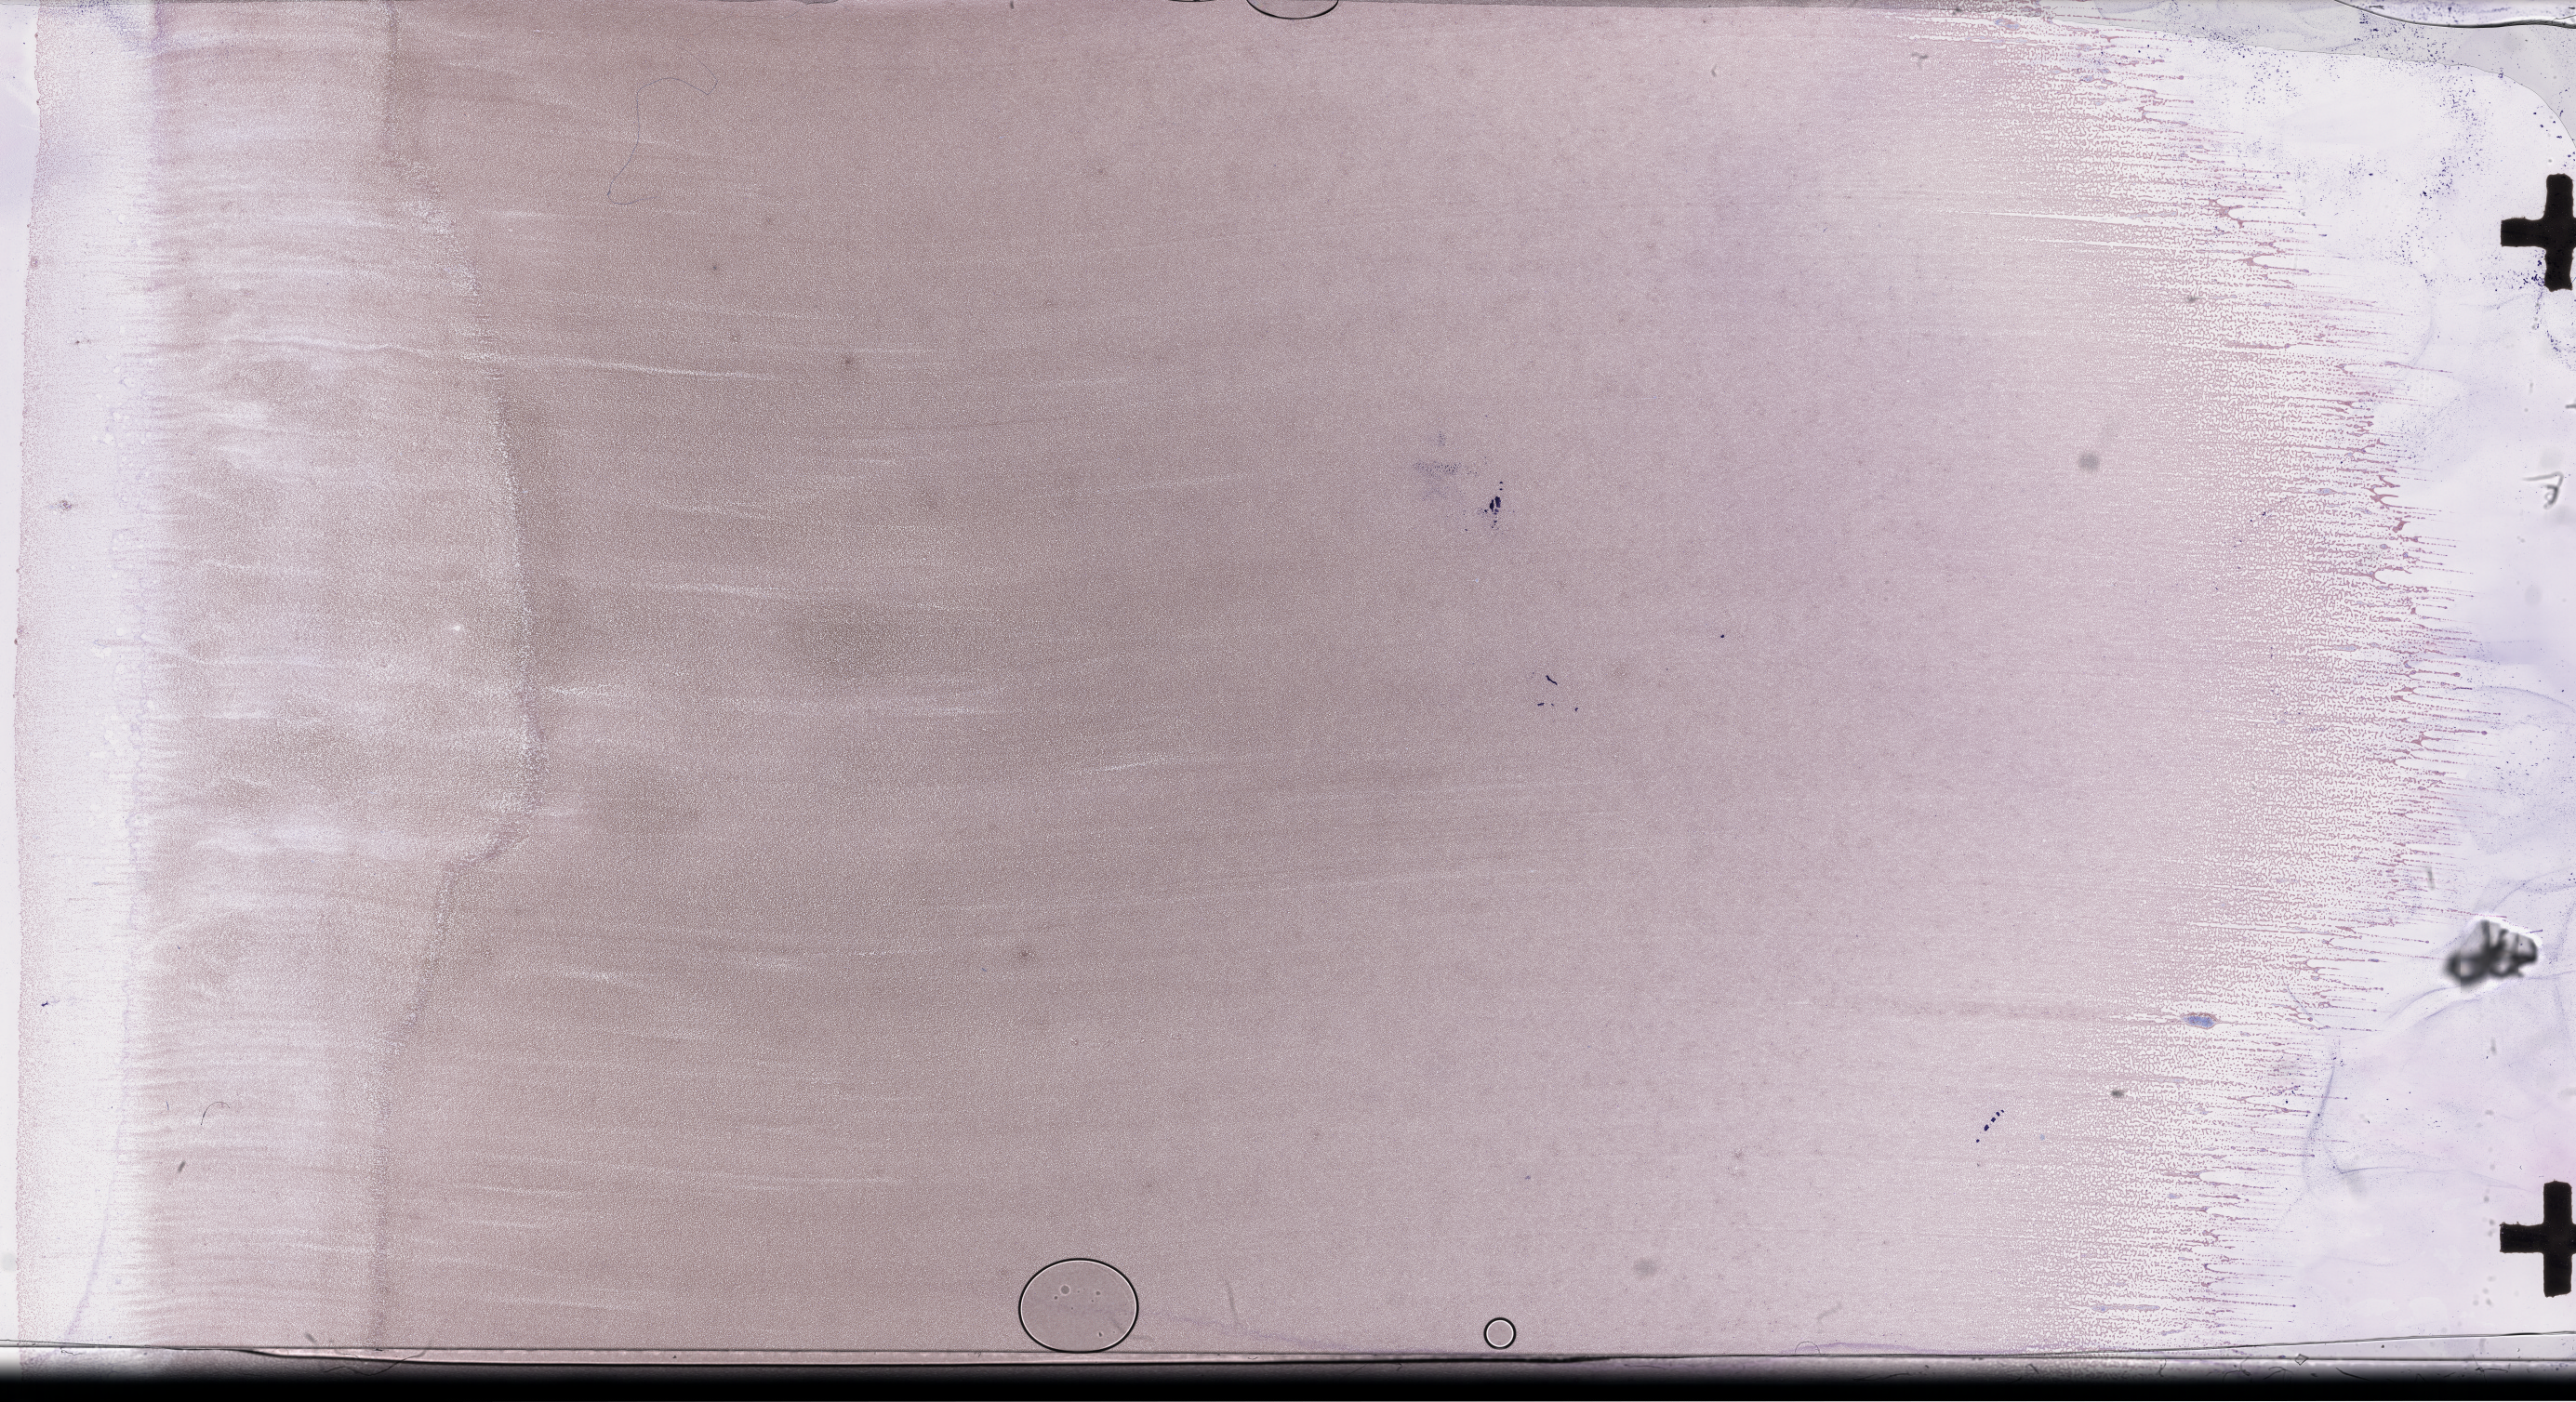
Wright-Giemsa-stained whole blood smear, whole-slide image — shown as a low-resolution overview of the whole scanned area (about 44.7 x 24.4 mm), EDTA-anticoagulated smear. Patient: male.
• patient diagnosis: Plasma Cell Myeloma